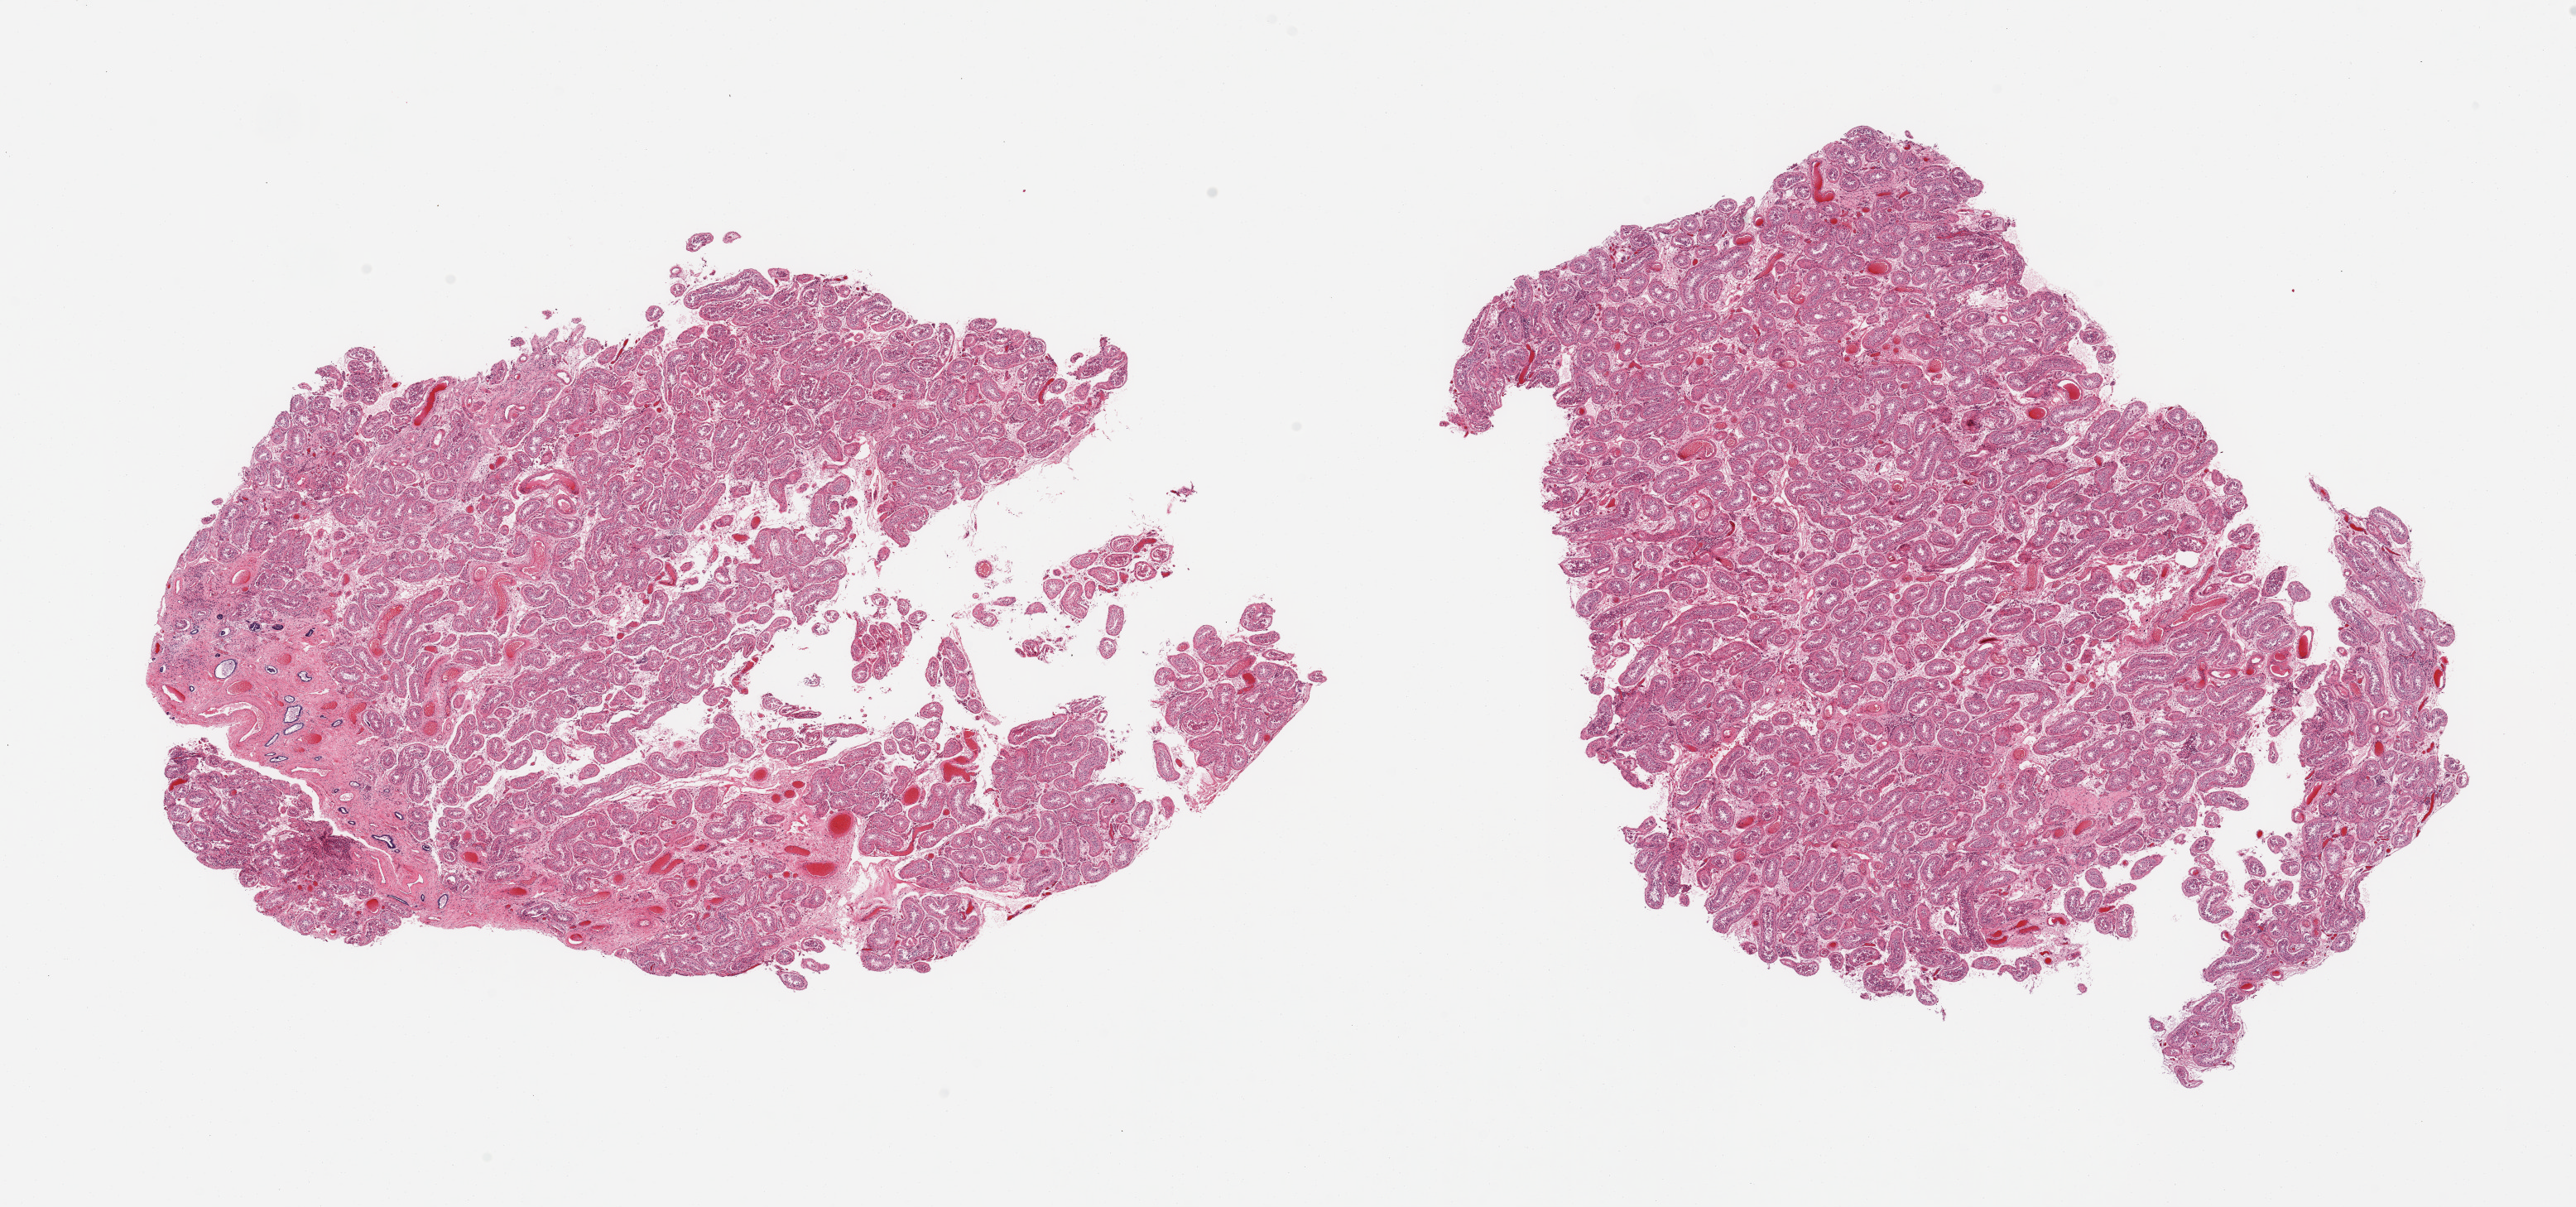
Digitized H&E-stained section — a low-resolution overview of the entire scanned area, about 24.6 x 11.5 mm. PAXgene-fixed, paraffin-embedded tissue. Target tissue: testis. Tissue donor sample. Donor: male.
- review note (as recorded): 2 pieces, spermatogenesis markedly reduced